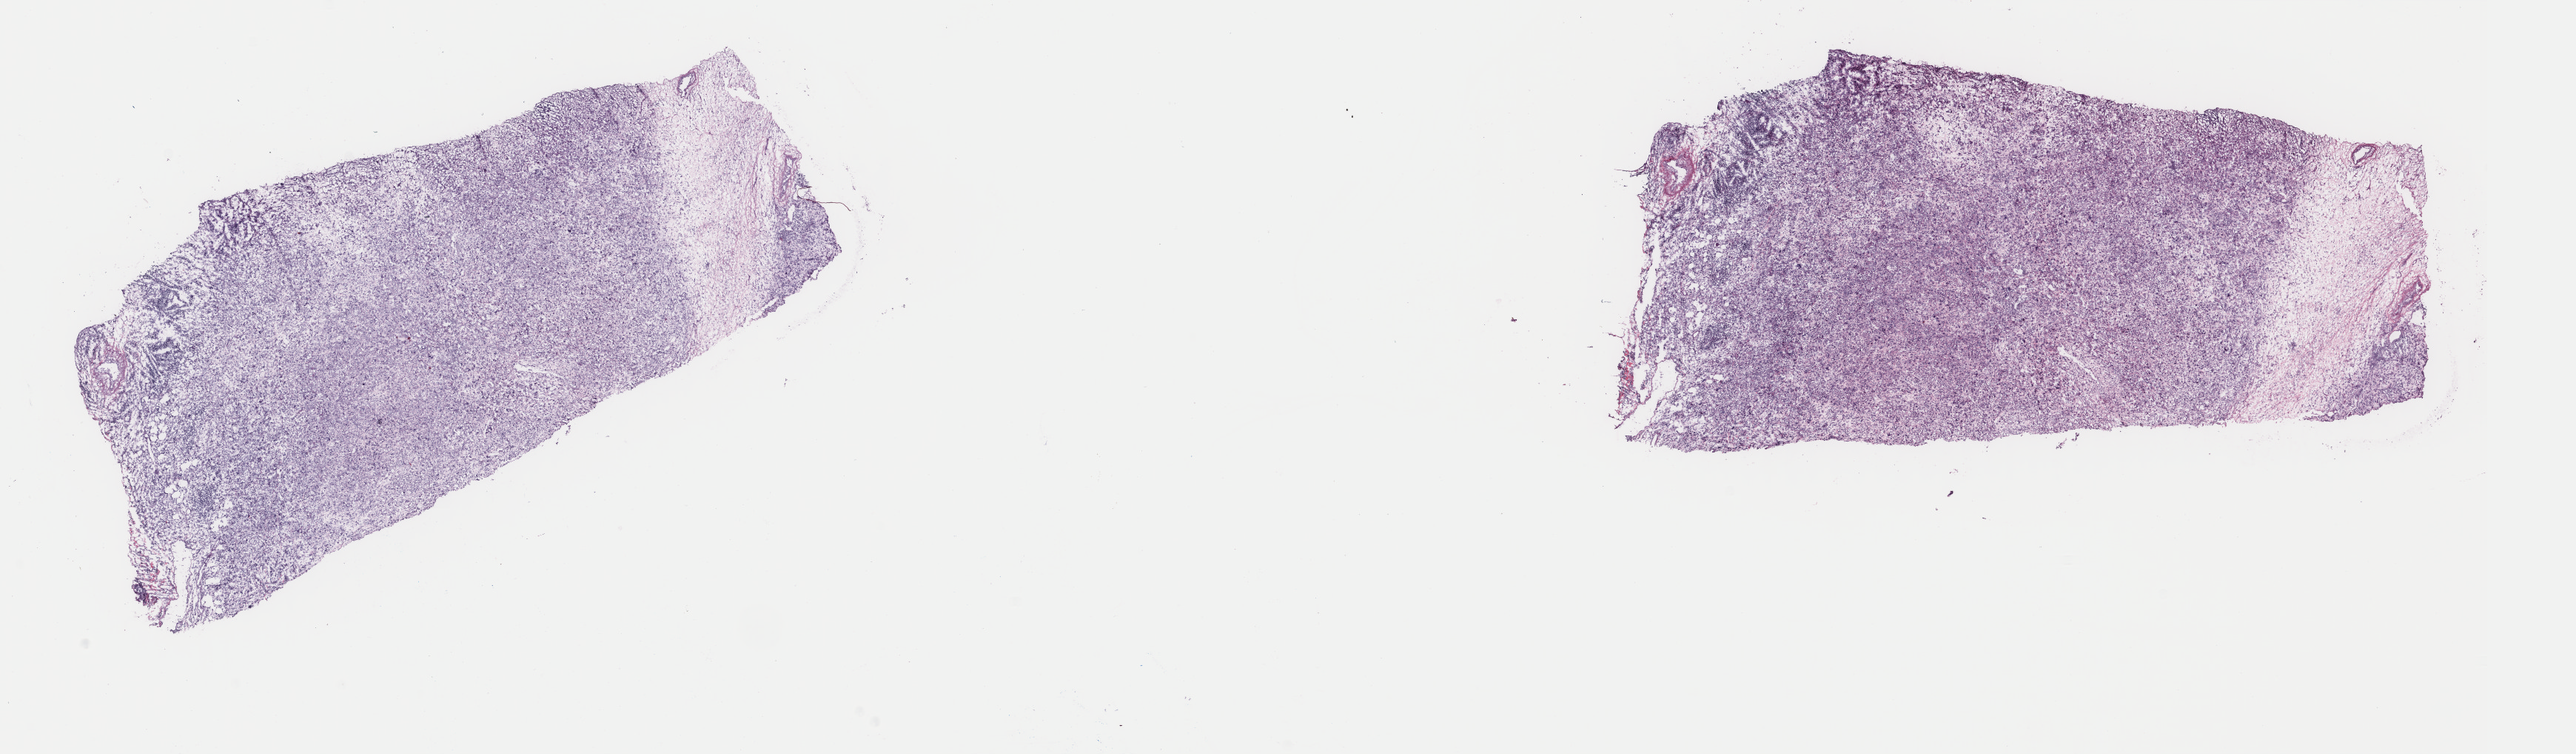
H&E whole-slide image, low-resolution overview of the scanned area, about 27.6 x 8.1 mm (from a 40x scan). Frozen section from the top of the tissue portion. Primary tumour sample from the connective, subcutaneous and other soft tissues. Patient sex: female. Slide review estimates, as recorded: tumour cells 85%, tumour nuclei 90%, normal cells 0%, stromal cells 15%, necrosis 0%. Inflammatory infiltration, as recorded: lymphocyte infiltration 8%, monocyte infiltration 2%, neutrophil infiltration 0%.
* histologic diagnosis: Pleomorphic liposarcoma (connective, subcutaneous and other soft tissues of lower limb and hip)